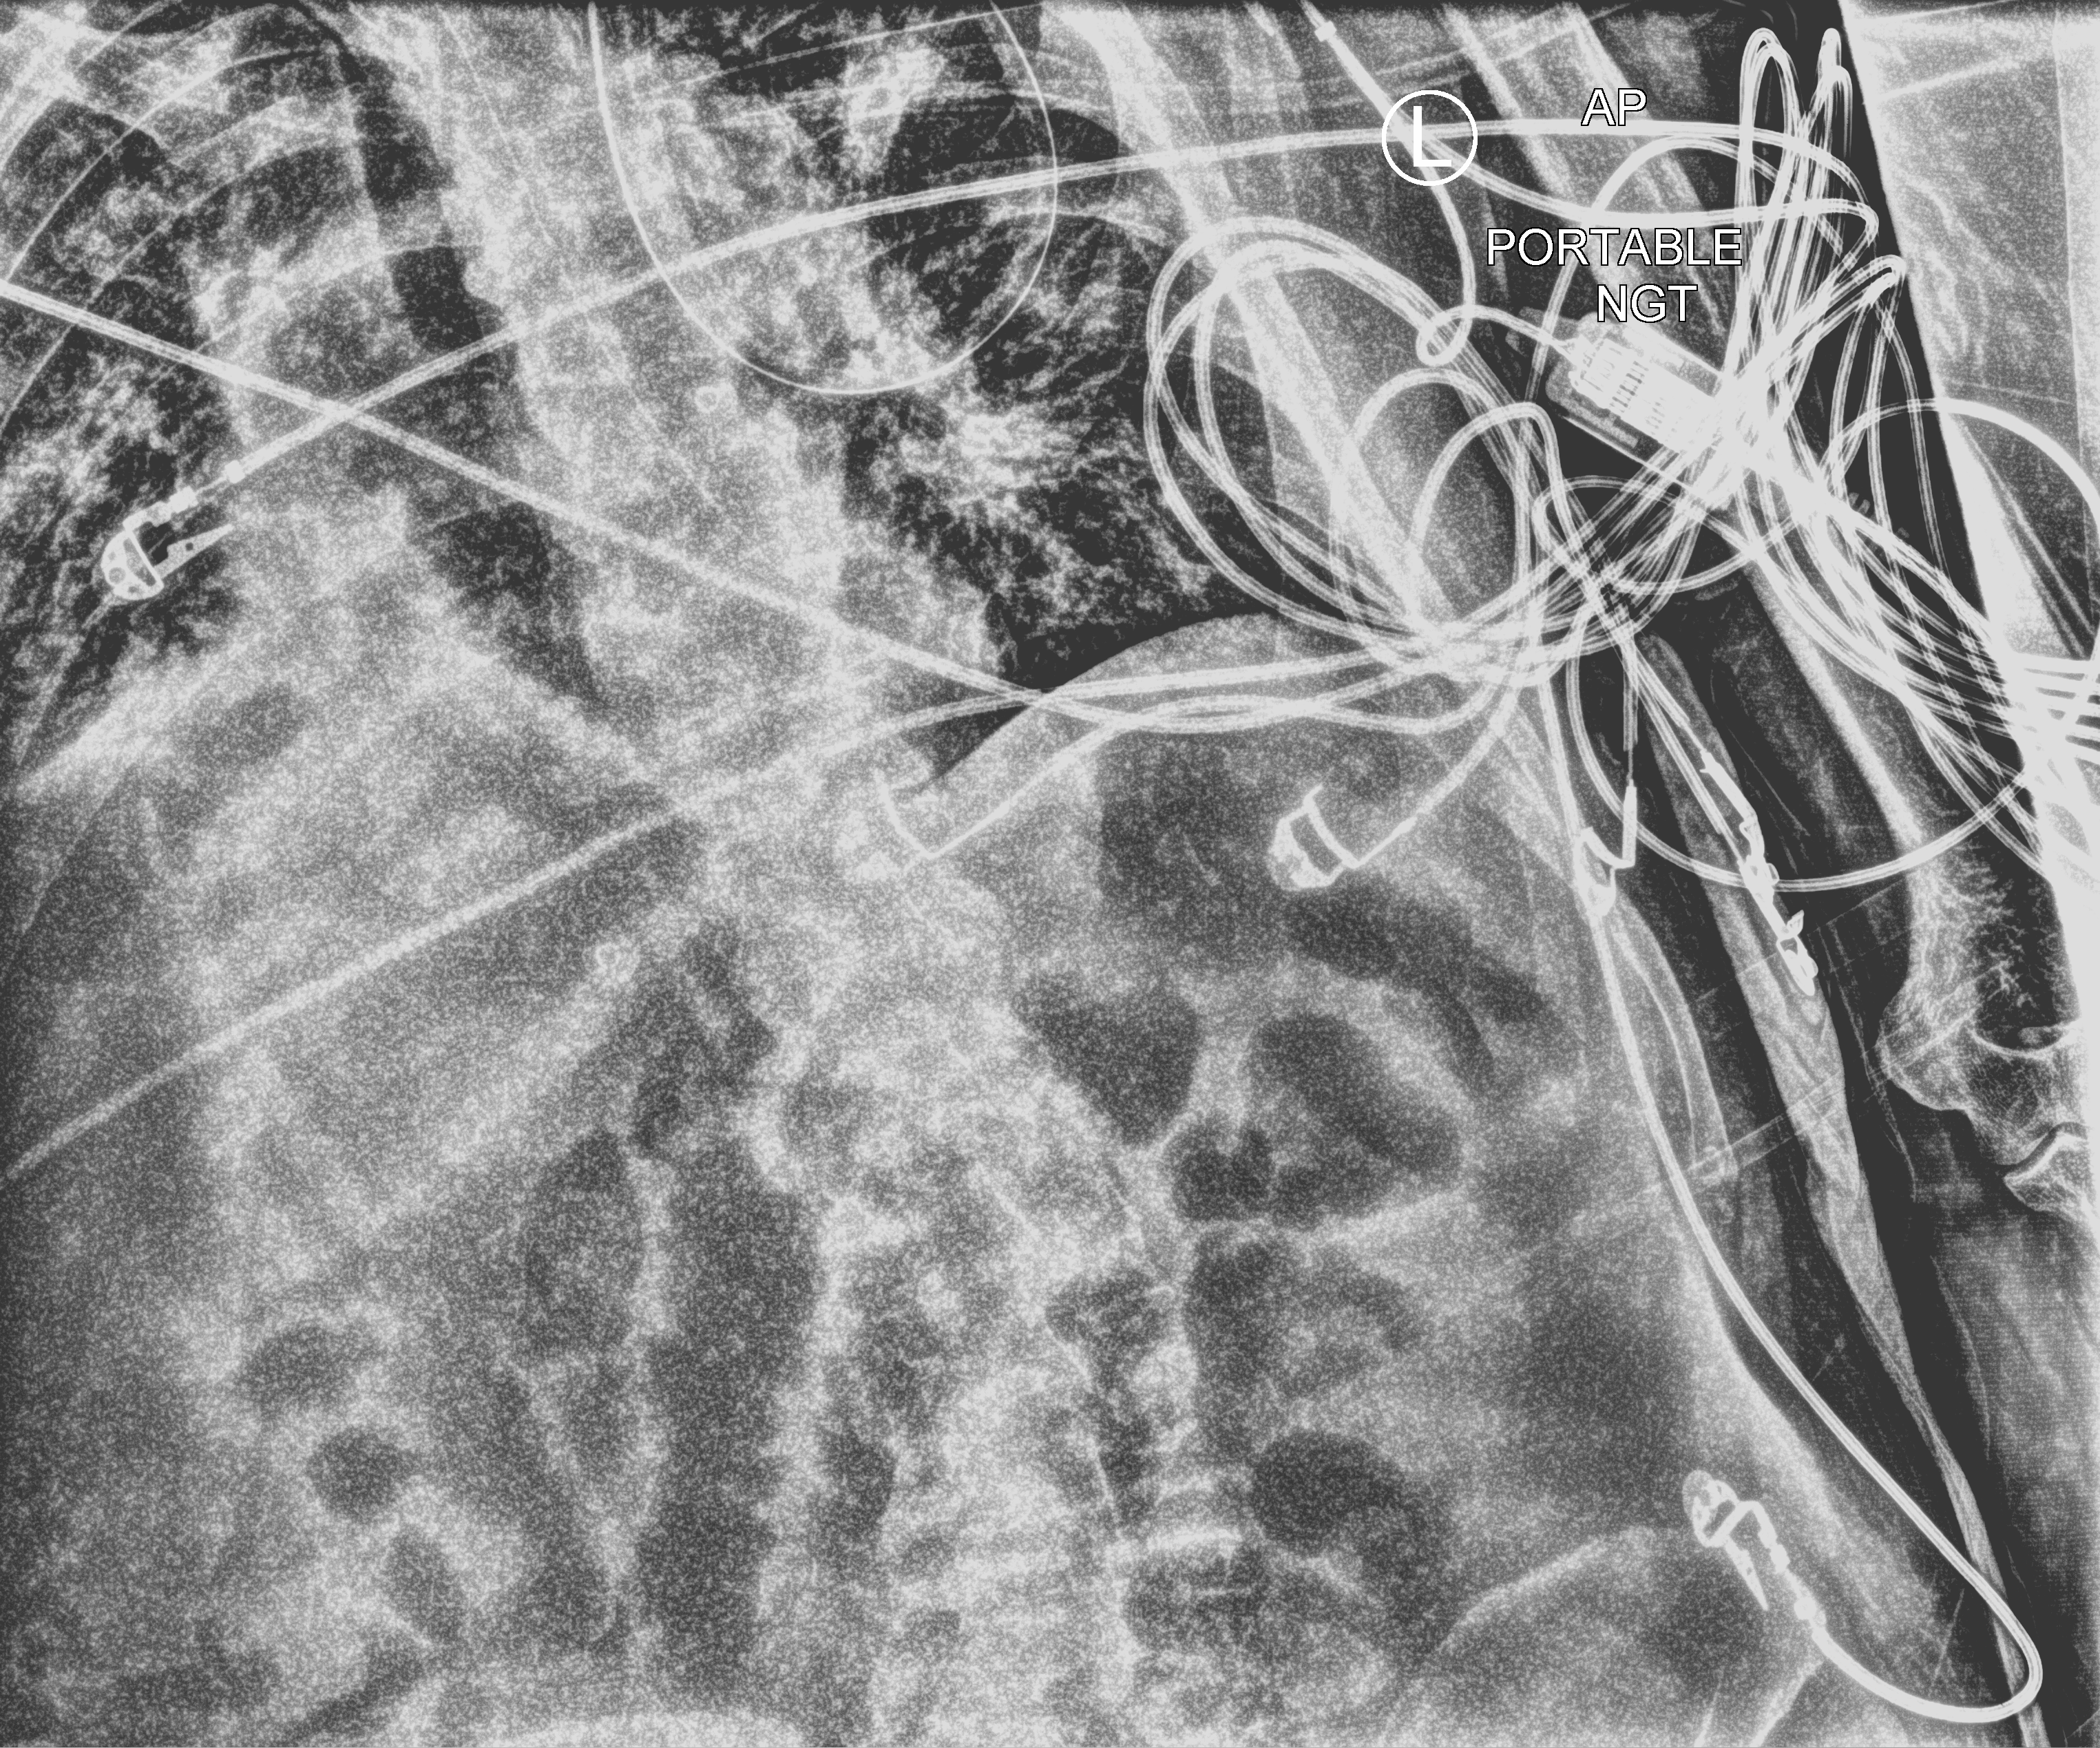
Bedside chest radiograph (computed radiography); anteroposterior (AP) projection. Patient hospitalised with COVID-19; male, aged 75–90 years.
Admission-level facts for this patient (not findings on this image; timing relative to this image not recorded): mechanically ventilated during this hospital stay: no.